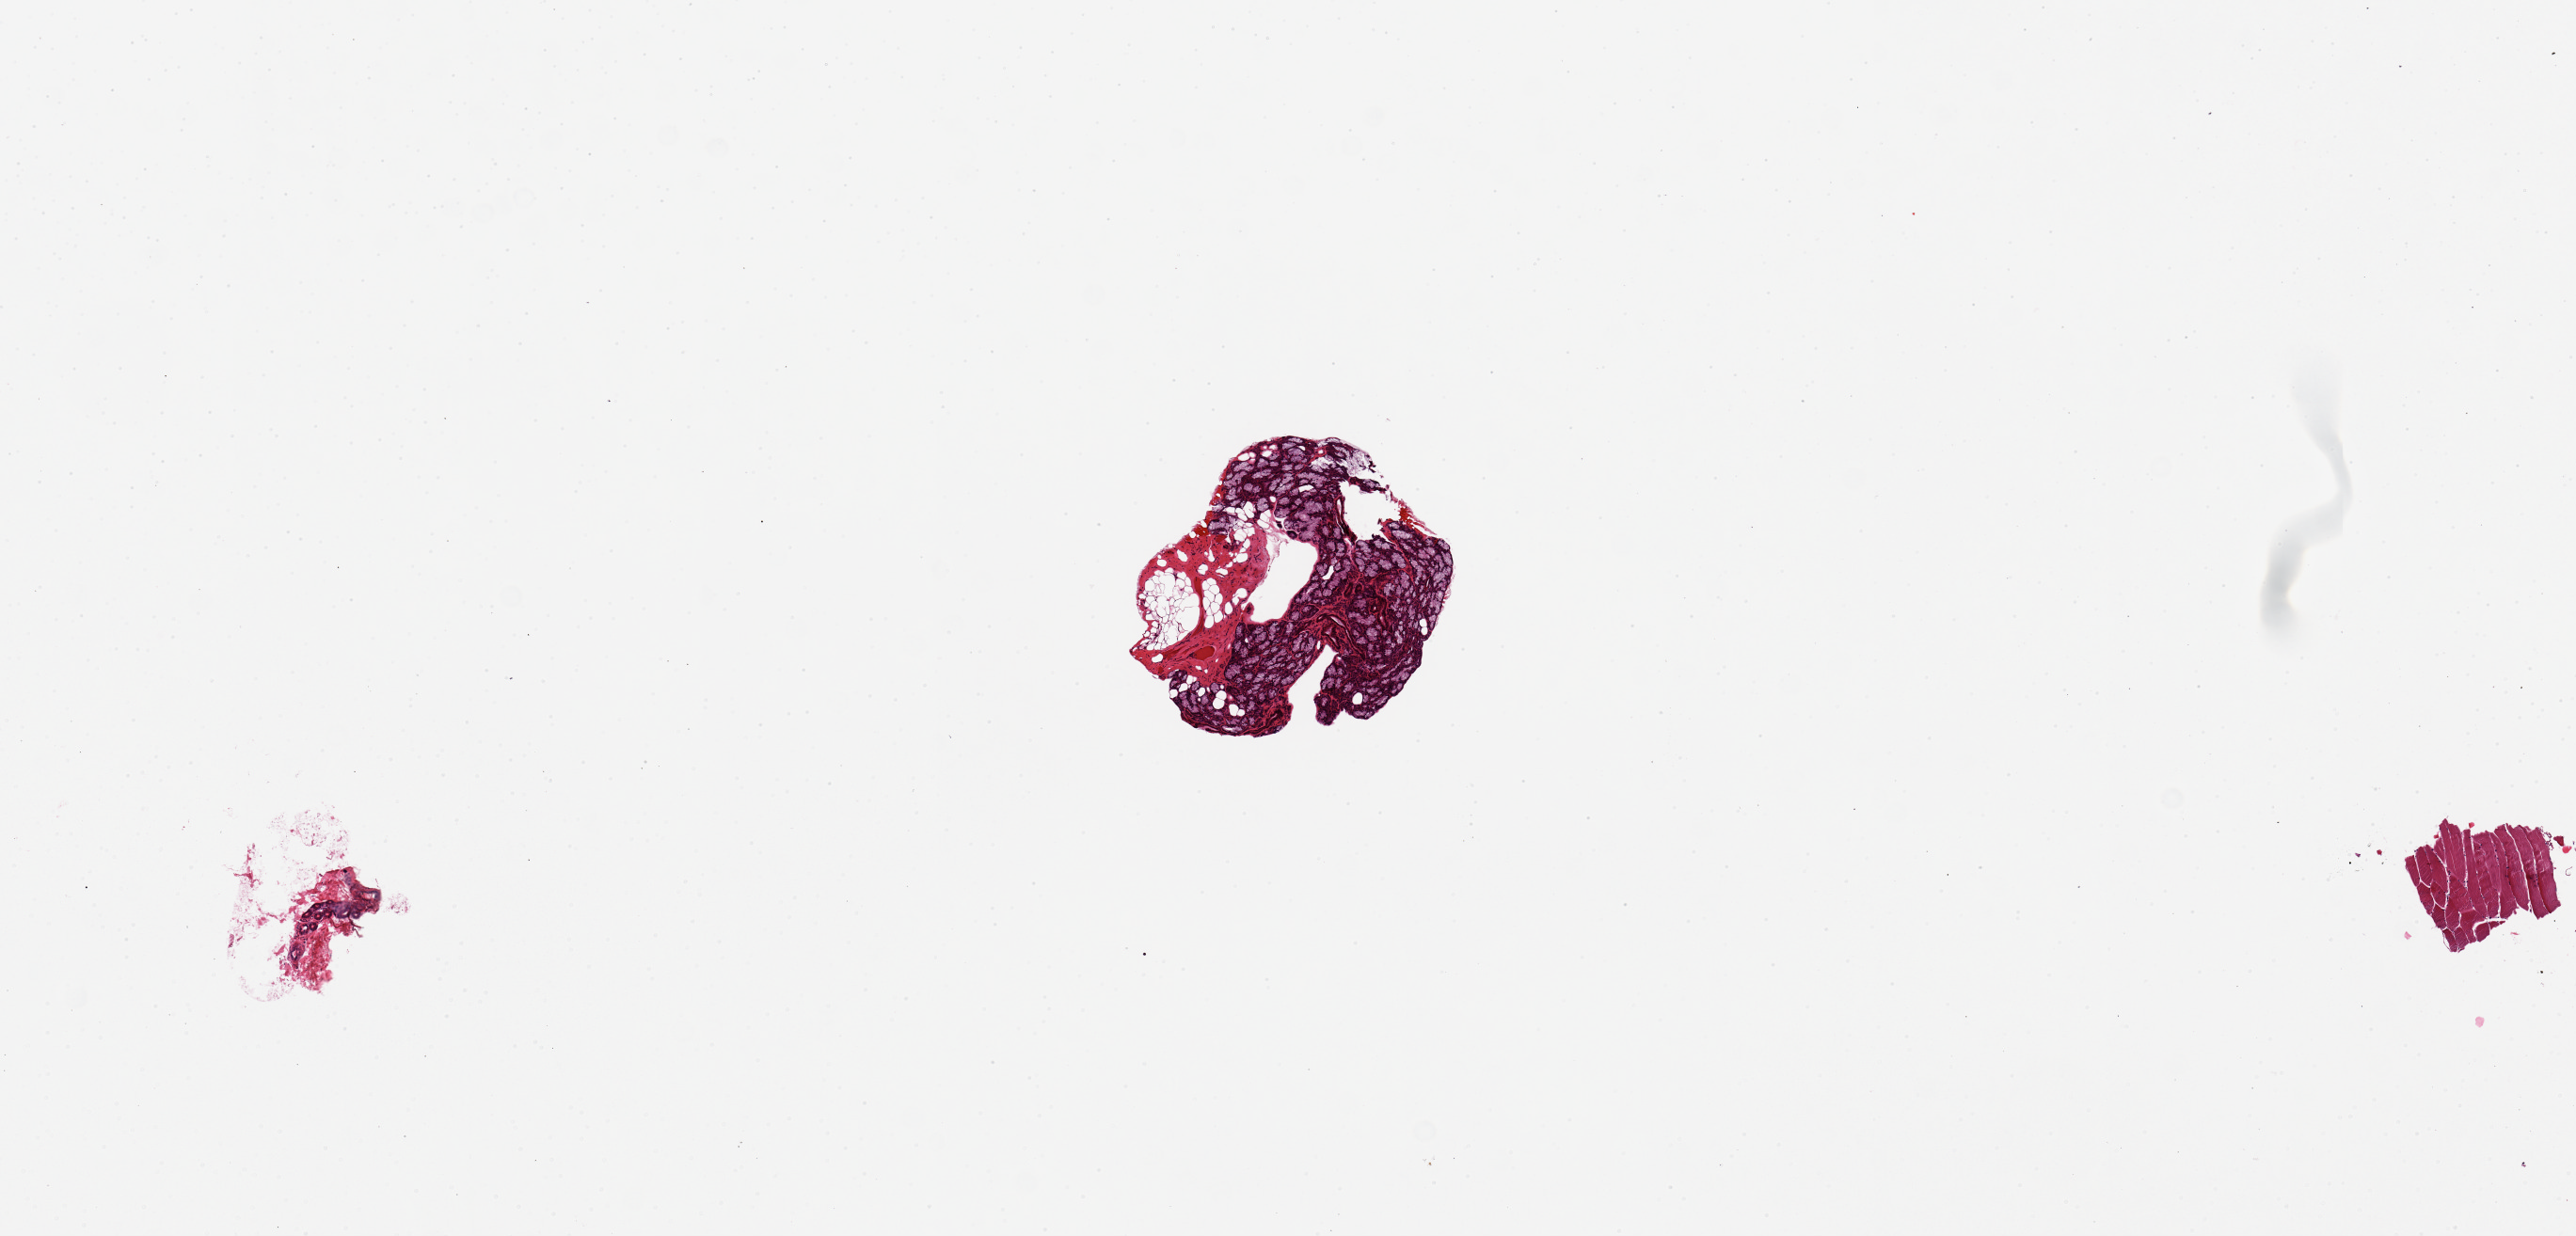
Haematoxylin and eosin whole-slide image — a low-resolution overview of the entire scanned area, about 10.8 x 5.2 mm. PAXgene-fixed paraffin-embedded (PFPE) section. Target tissue: minor salivary gland. Tissue donor sample. Male donor.
* review note (as recorded): 3 pieces, 2 minute muscle/stroma, one (1.3x1.2mm) is ~80% glandular tissue, appears dessicated